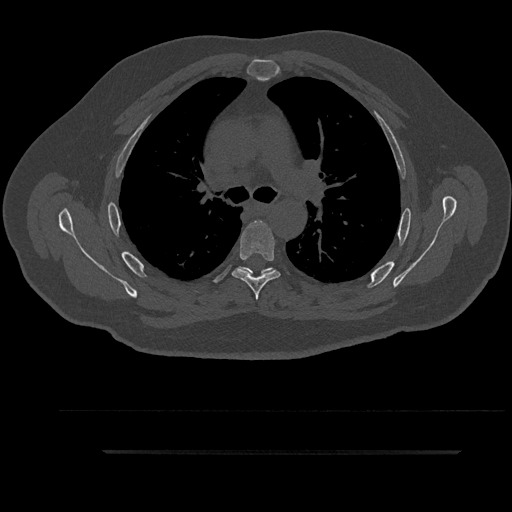
CT including the spine, one axial slice; position 623 of 797 along the scan axis; reconstruction kernel Br40s/3; bone window (W 1800 / L 400 HU); 512 × 512 image matrix, field of view 432 × 432 mm. Patient: male, 63 years. From the clinical record (not read from this slice): primary cancer: renal; vertebrae with lytic lesions (as recorded): T8.
Annotated regions visible in this slice (semi-automatically segmented with operator editing):
- T5 vertebra: bounding box [x1, y1, x2, y2] px = [232, 221, 281, 300]
- T6 vertebra: [242, 268, 275, 277]